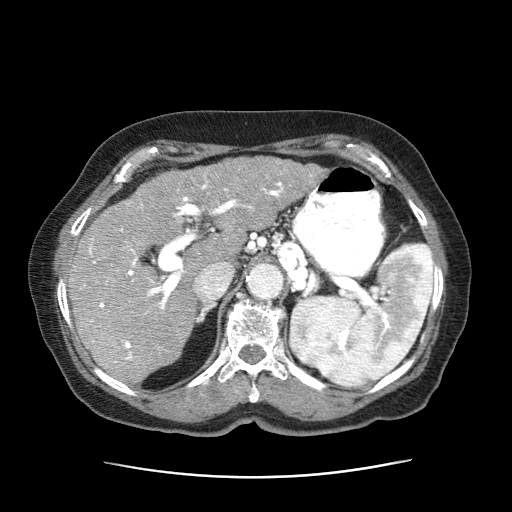
Contrast-enhanced abdominal CT (liver protocol), one axial slice; 120 kVp; intravenous contrast given; soft-tissue window (W 400 / L 40 HU); 2.5 mm slice thickness; 512 × 512 image matrix, field of view 360 × 360 mm. Female patient, age 79 years. Case-level facts recorded for this patient, not image findings: diagnosis: hepatocellular carcinoma (patient treated with transarterial chemoembolisation; whether this scan precedes or follows treatment is not stated here); TNM stage (as recorded): Stage-II; Child-Pugh class: B; tumour nodularity: multinodular; tumour size: 5 cm.
Outlined on this slice (semi-automatically segmented with operator editing):
- abdominal aorta: bounding box <247,265,283,300> (left, top, right, bottom; pixels)
- liver parenchyma outside the tumour (the mass and vessels are separate outlines, so this box may not span the whole liver): <67,171,249,388>
- mass: <168,157,324,237>
- liver vessels: <79,182,291,361>